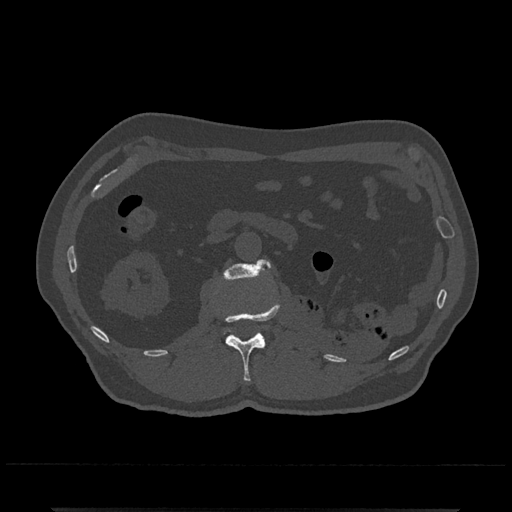
CT including the spine, one axial slice; position 338 of 797 along the scan axis; bone window (W 1800 / L 400 HU); 0.5 mm slice thickness; 512 × 512 image matrix. Patient: male, 67 years. From the clinical record (not read from this slice): primary cancer: prostate.
Structures marked on this image (semi-automatic segmentation, software-assisted and operator-edited):
- L1 vertebra: bounding box [x1, y1, x2, y2] px = [225, 304, 280, 382]
- L2 vertebra: [223, 259, 271, 280]